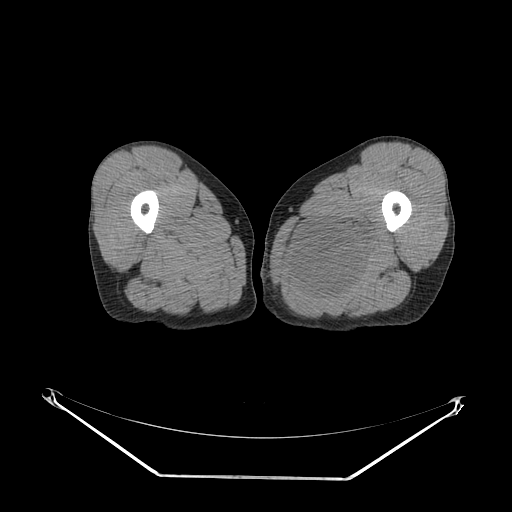
CT of an extremity soft-tissue mass (from a PET/CT study), one axial slice. Position 21 of 267 along the scan axis. Reconstruction kernel SOFT. Soft-tissue window (W 400 / L 40 HU). 3.75 mm slice thickness. 512 × 512 image matrix. Male patient. From the clinical record (not read from this slice): histological type: pleiomorphic liposarcoma; grade: high; site of the primary tumour: left thigh.
Structures marked on this image (expert contour drawn on MRI and transferred to this co-registered scan by the dataset authors):
- gross tumour volume including surrounding oedema: box from (x=292, y=210) to (x=384, y=305) px
- gross tumour volume (mass): (x=295, y=221)–(x=369, y=298)